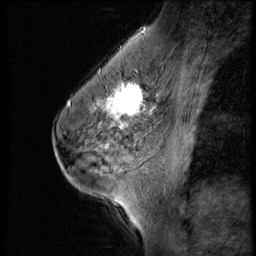
Breast MRI (dynamic contrast-enhanced), one sagittal slice; position 36 of 56 along the scan axis; 3 images stored at this slice position (order not interpretable as contrast timing); 1.5 T; TE 4.2 ms, TR 9 ms; 2.5 mm slice thickness; 256 × 256 image matrix, field of view 180 × 180 mm. Patient: female, 45 years. Case-level facts recorded for this patient, not image findings: setting: breast cancer imaged before/during neoadjuvant chemotherapy; receptor status: HR-positive, HER2-negative.
Structures marked on this image (semi-automatically segmented with operator editing):
- analysis volume of interest (the breast-tissue region the enhancement analysis was run in; not a lesion): box from (x=102, y=77) to (x=166, y=129) px
- tumour enhancement mask (voxels above the 140 % enhancement threshold inside the analysis volume of interest): (x=102, y=82)–(x=154, y=129)